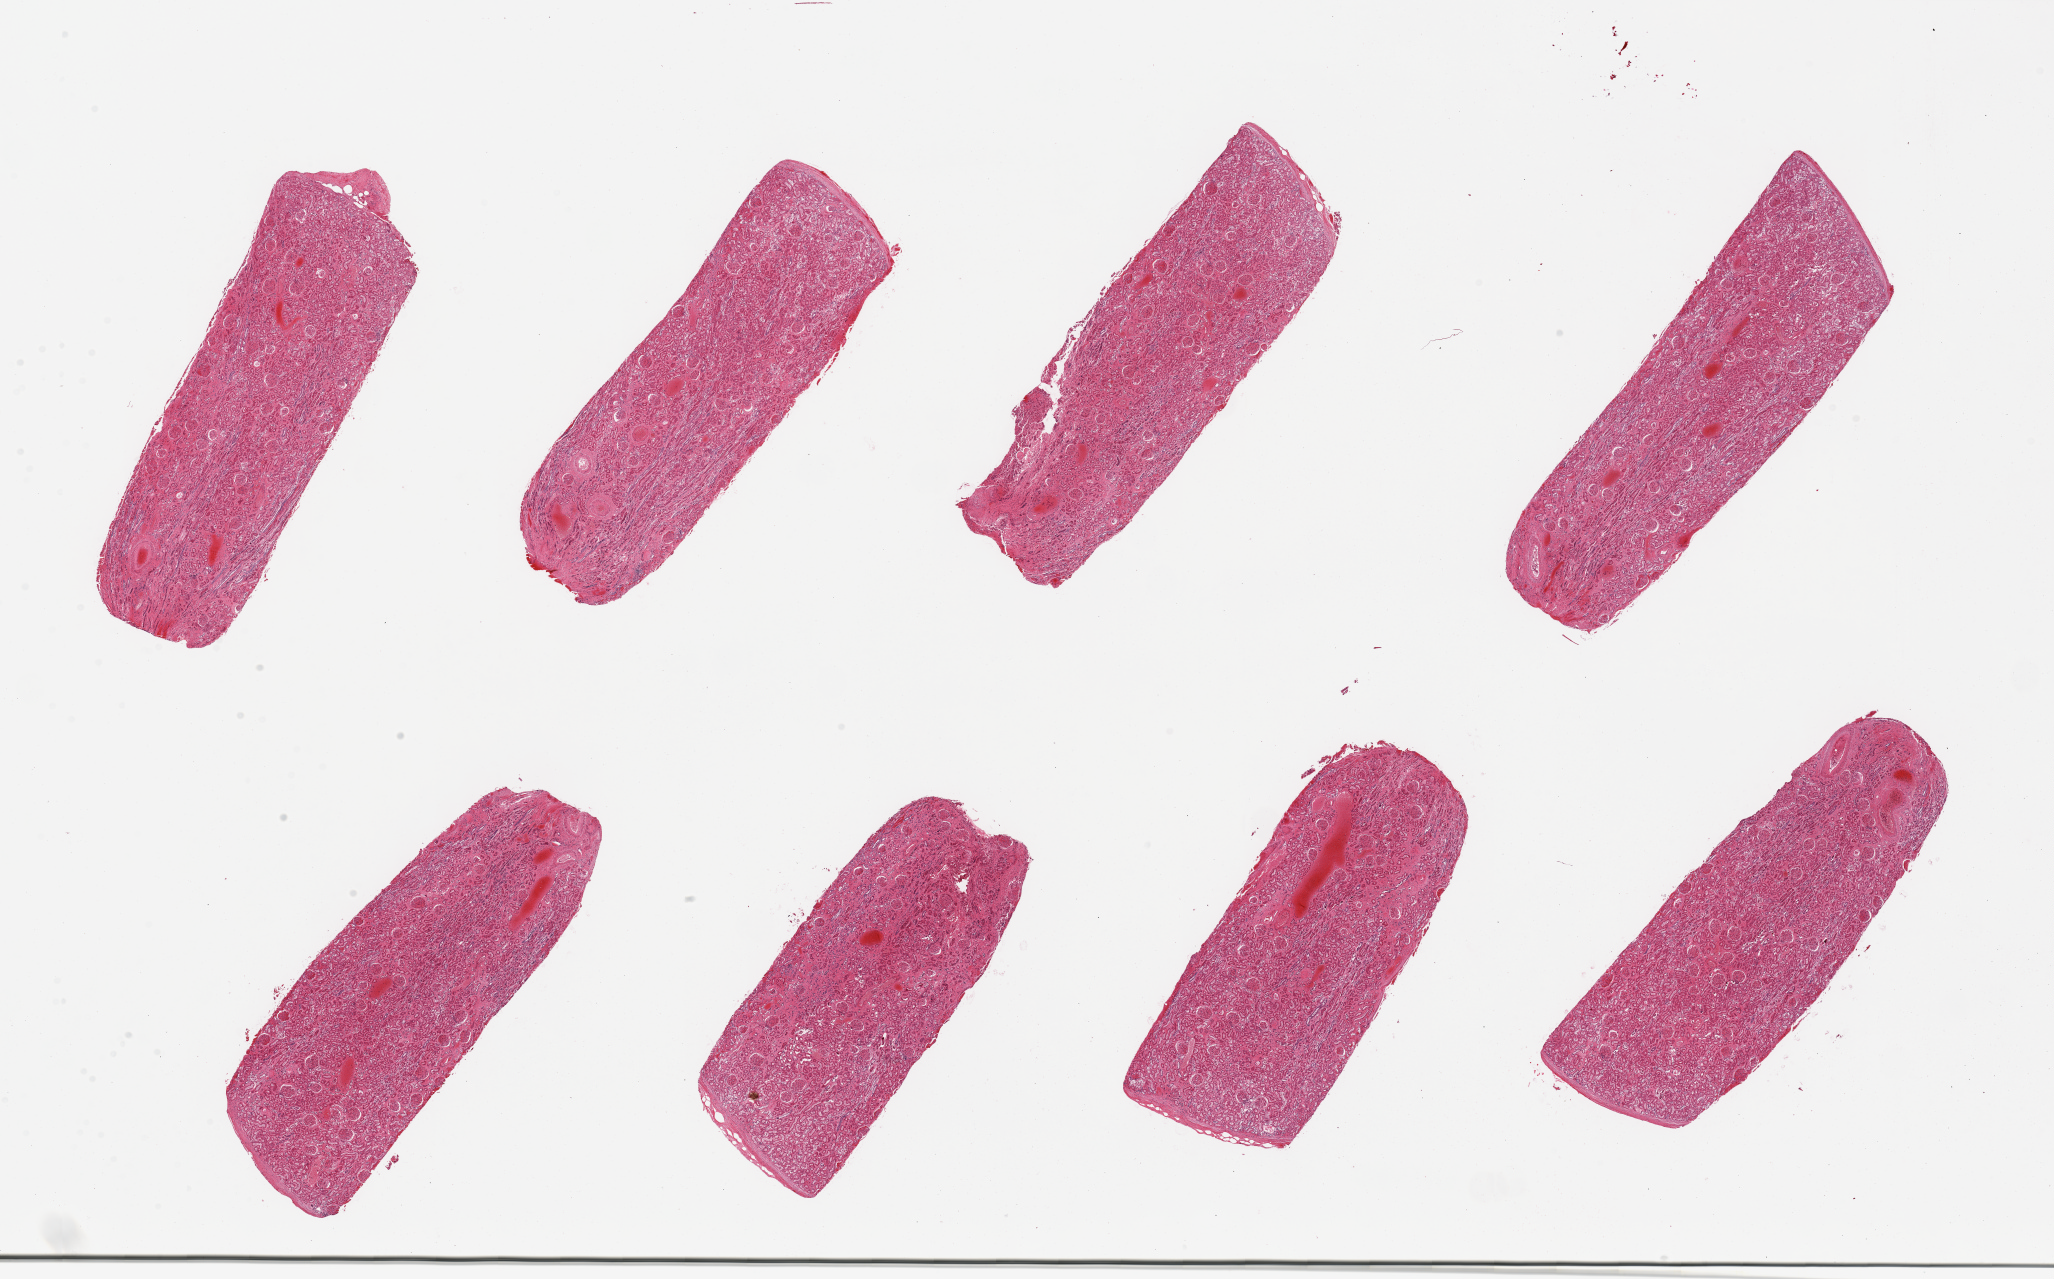
Whole-slide image, hematoxylin and eosin (H&E) stain — low-resolution overview of the scanned area, about 32.5 x 20.2 mm (from a 20x scan). PAXgene-fixed paraffin-embedded (PFPE) section. Sampled site (target tissue): renal cortex. Donor tissue sample. Donor sex: male.
Review note (as recorded): 8 pieces, glomeruli present; tubular autolysis moderately advanced.